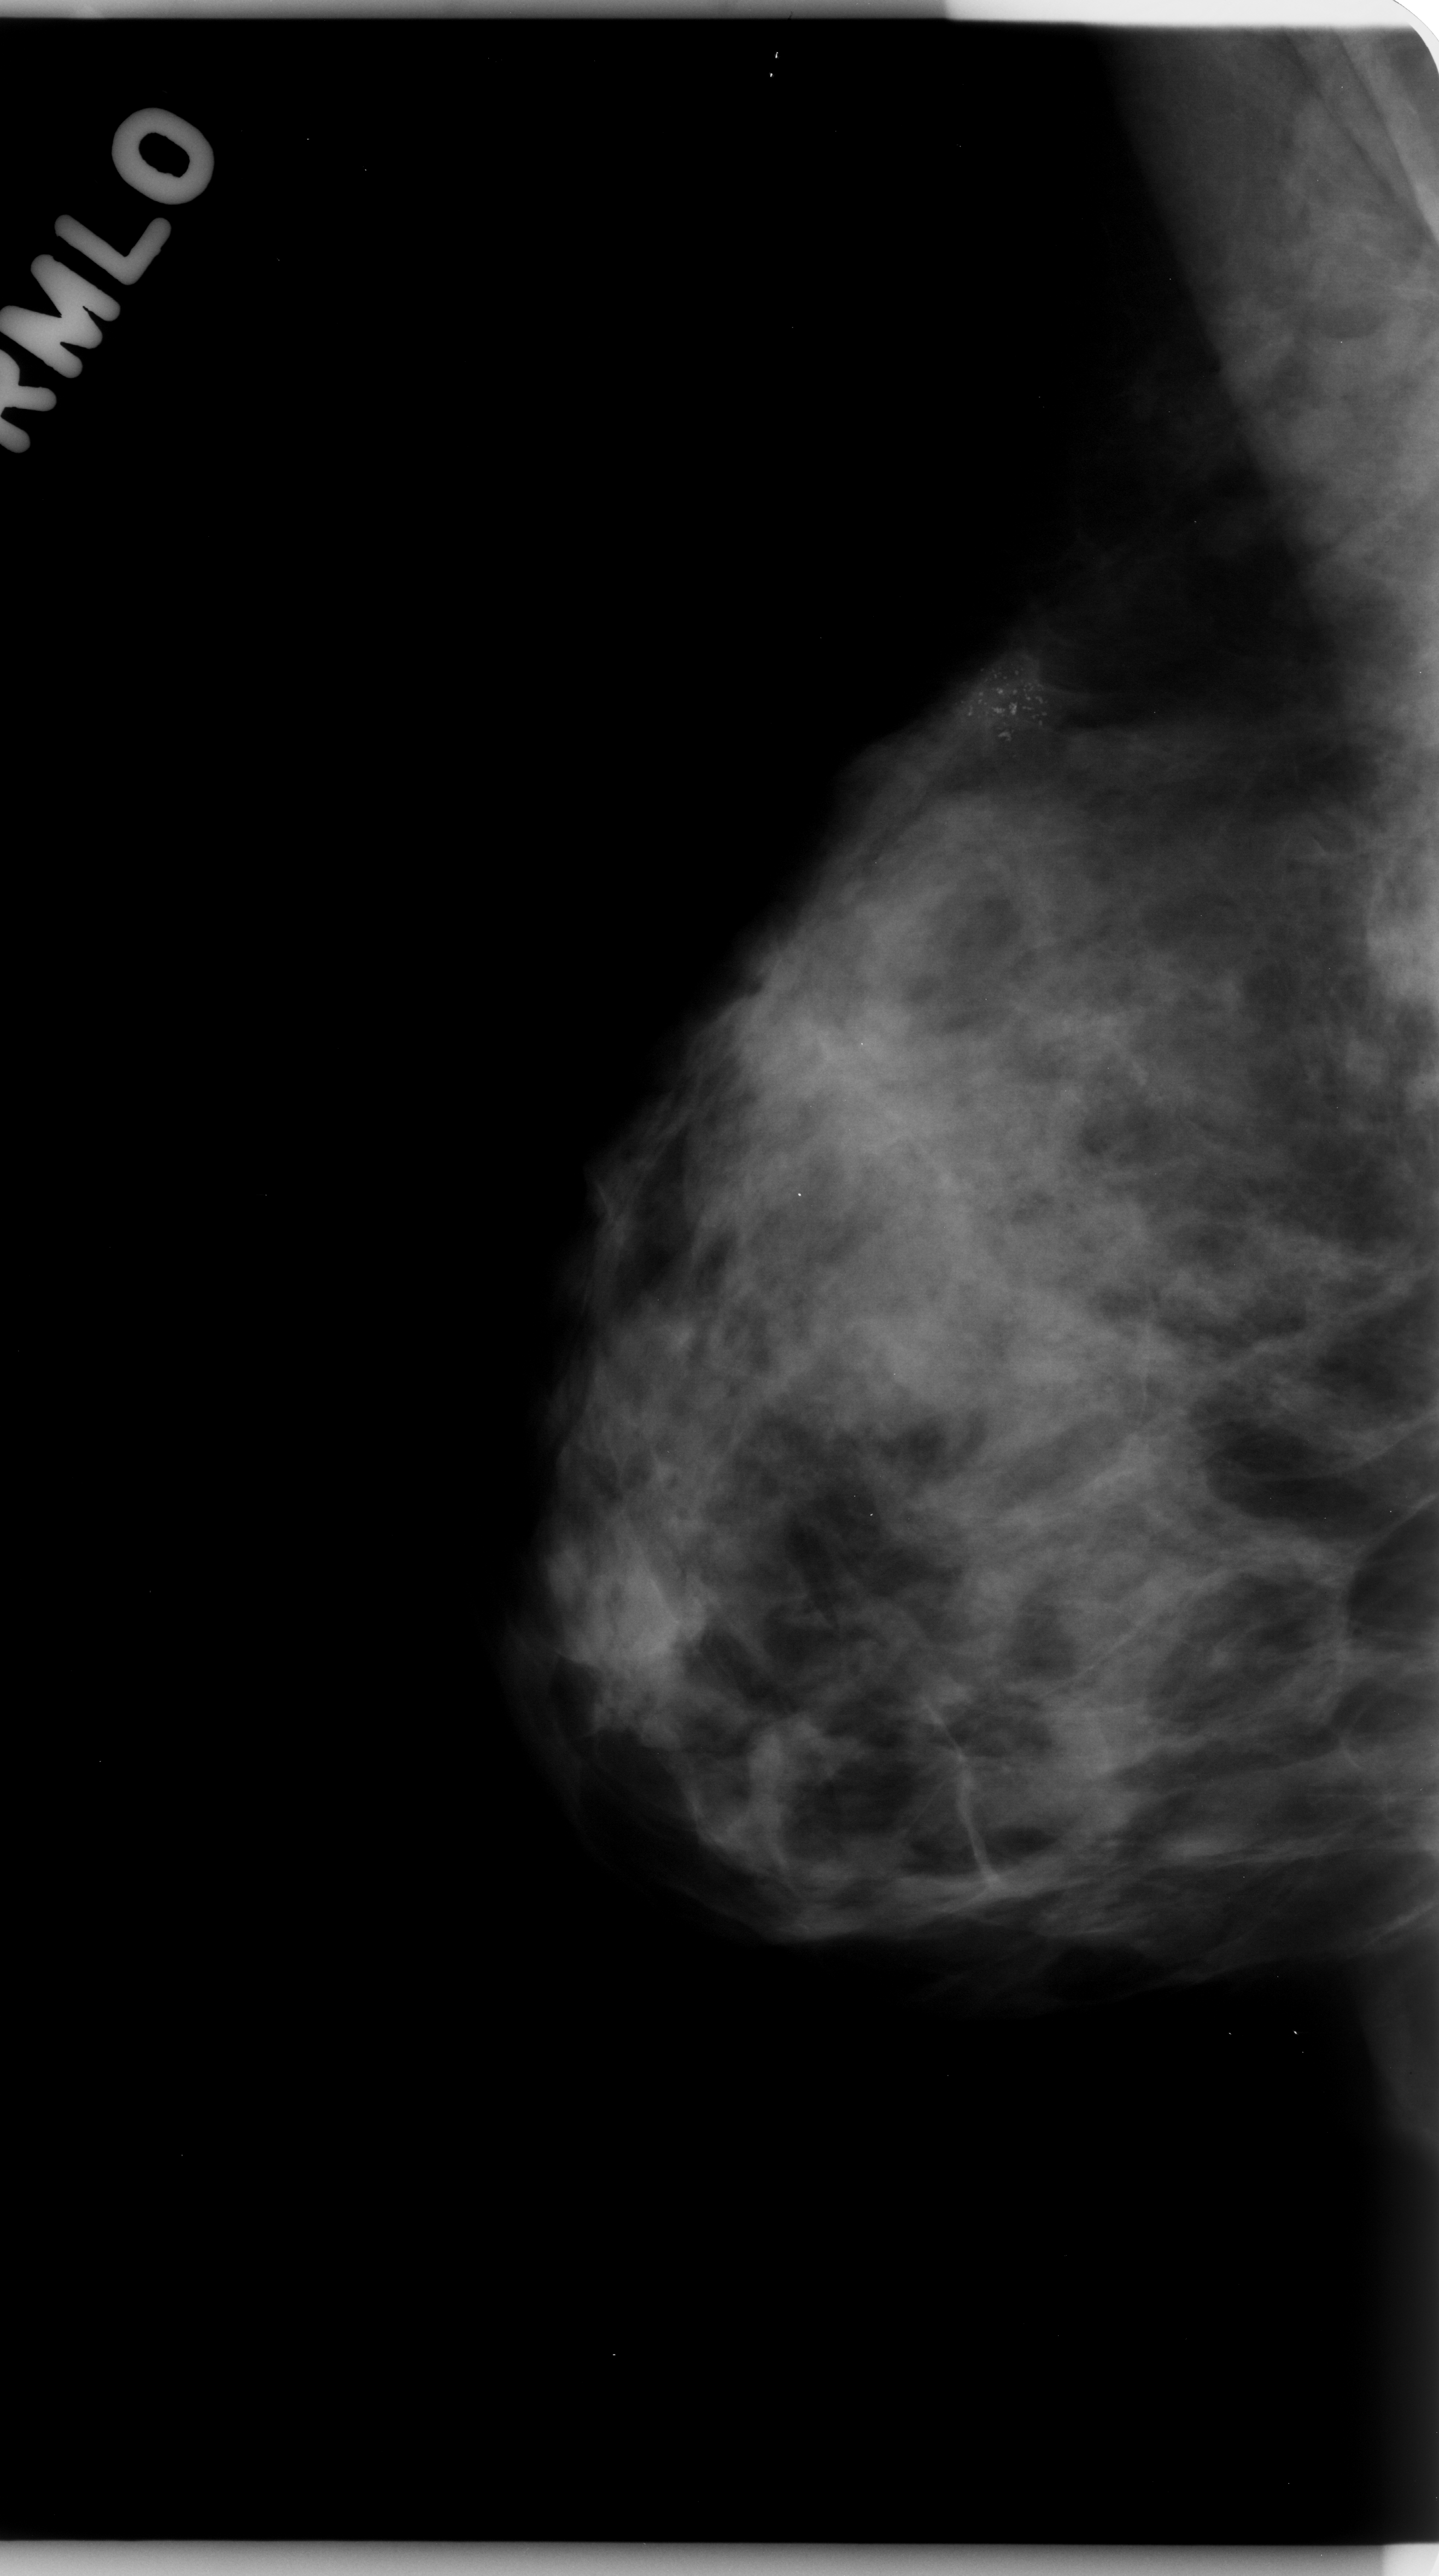
Scanned film-screen mammogram. Right breast. Mediolateral oblique (MLO) view. Breast composition: heterogeneously dense (BI-RADS density category 3 of 4). 1439 × 2576 image matrix.
Expert-marked regions of interest on this film, with their recorded descriptors:
- calcifications, morphology pleomorphic, distribution clustered; BI-RADS assessment category 5; pathology result (as recorded, not read from the image): malignant: bounding box <936,634,1068,758> (left, top, right, bottom; pixels)